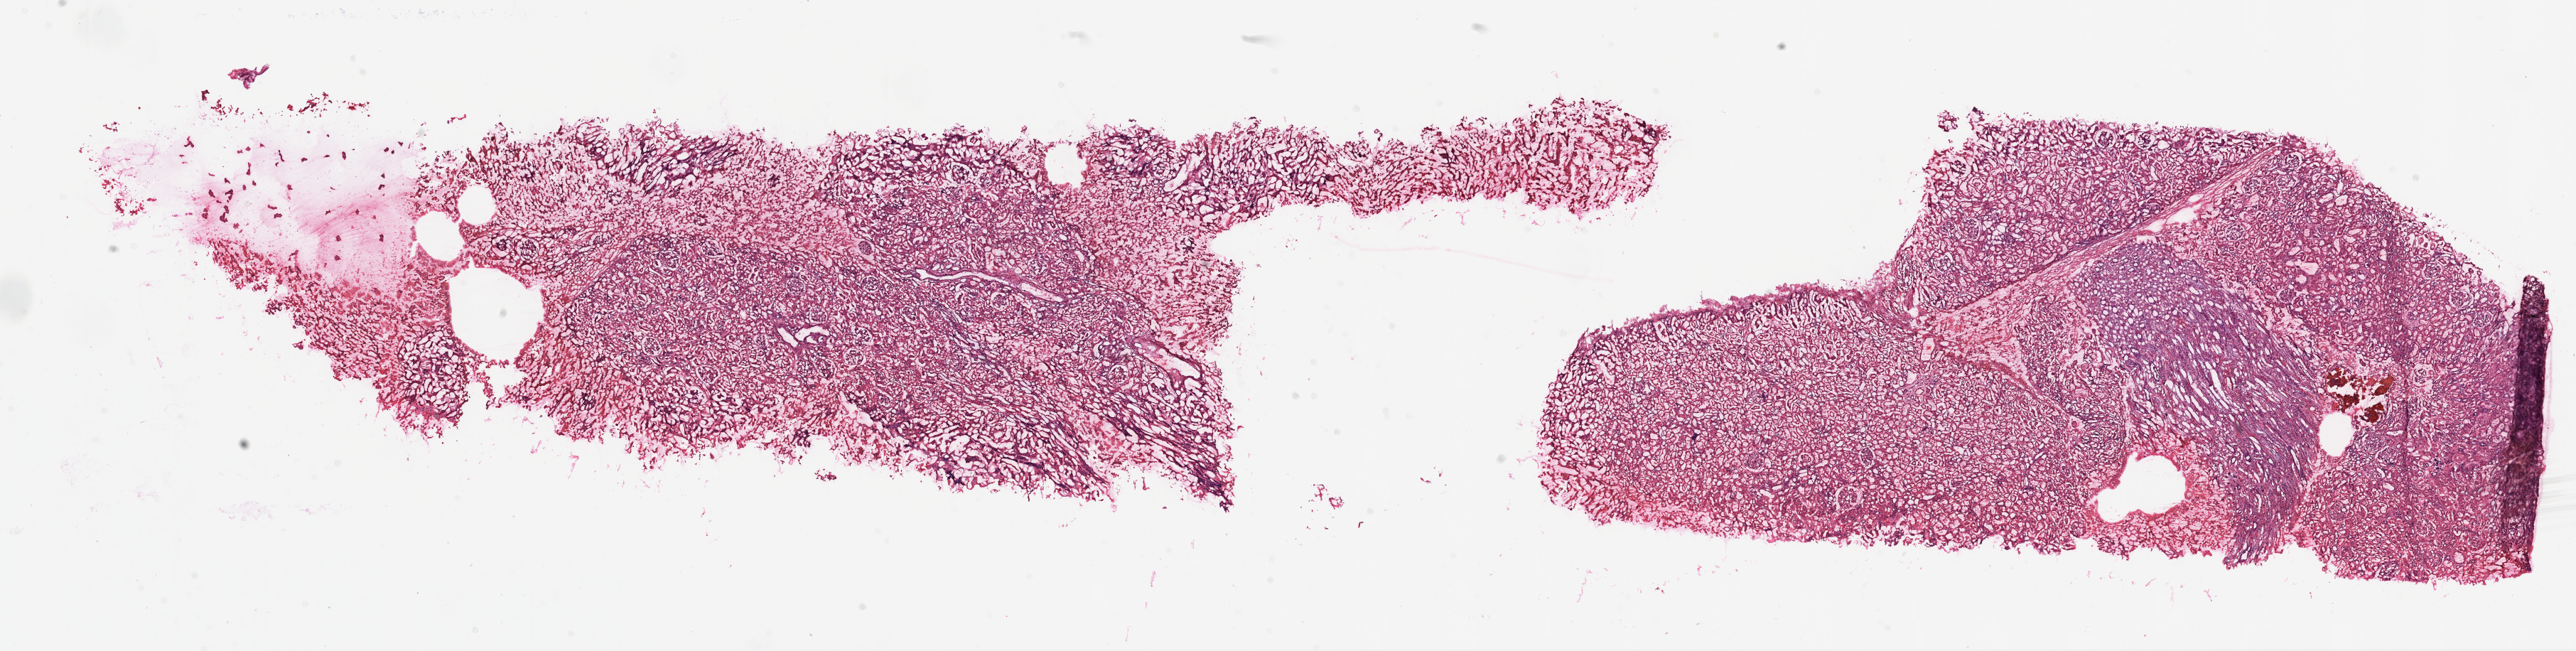
H&E whole-slide image, a low-resolution overview of the entire scanned area, about 29.1 x 7.4 mm. Frozen section from the top of the tissue portion. Solid tissue normal (non-tumour tissue) sample from the kidney. Male patient; age at initial diagnosis 57 years.
* this section: solid tissue normal (non-tumour) sample from the same patient
* patient diagnosis: Clear cell adenocarcinoma, NOS